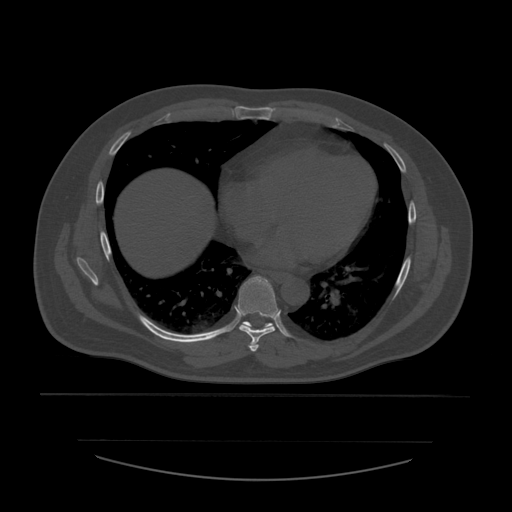
CT including the spine, one axial slice; position 353 of 532 along the scan axis; reconstruction kernel STANDARD; bone window (W 1800 / L 400 HU); 1.25 mm slice thickness; 512 × 512 image matrix, field of view 441 × 441 mm. Patient age 44 years. Case-level facts recorded for this patient, not image findings: primary cancer: soft tissue sarcoma.
Annotated regions visible in this slice (semi-automatically segmented with operator editing):
- T6 vertebra: box from (x=248, y=341) to (x=259, y=353) px
- T7 vertebra: (x=238, y=276)–(x=280, y=343)
- T8 vertebra: (x=242, y=322)–(x=274, y=331)